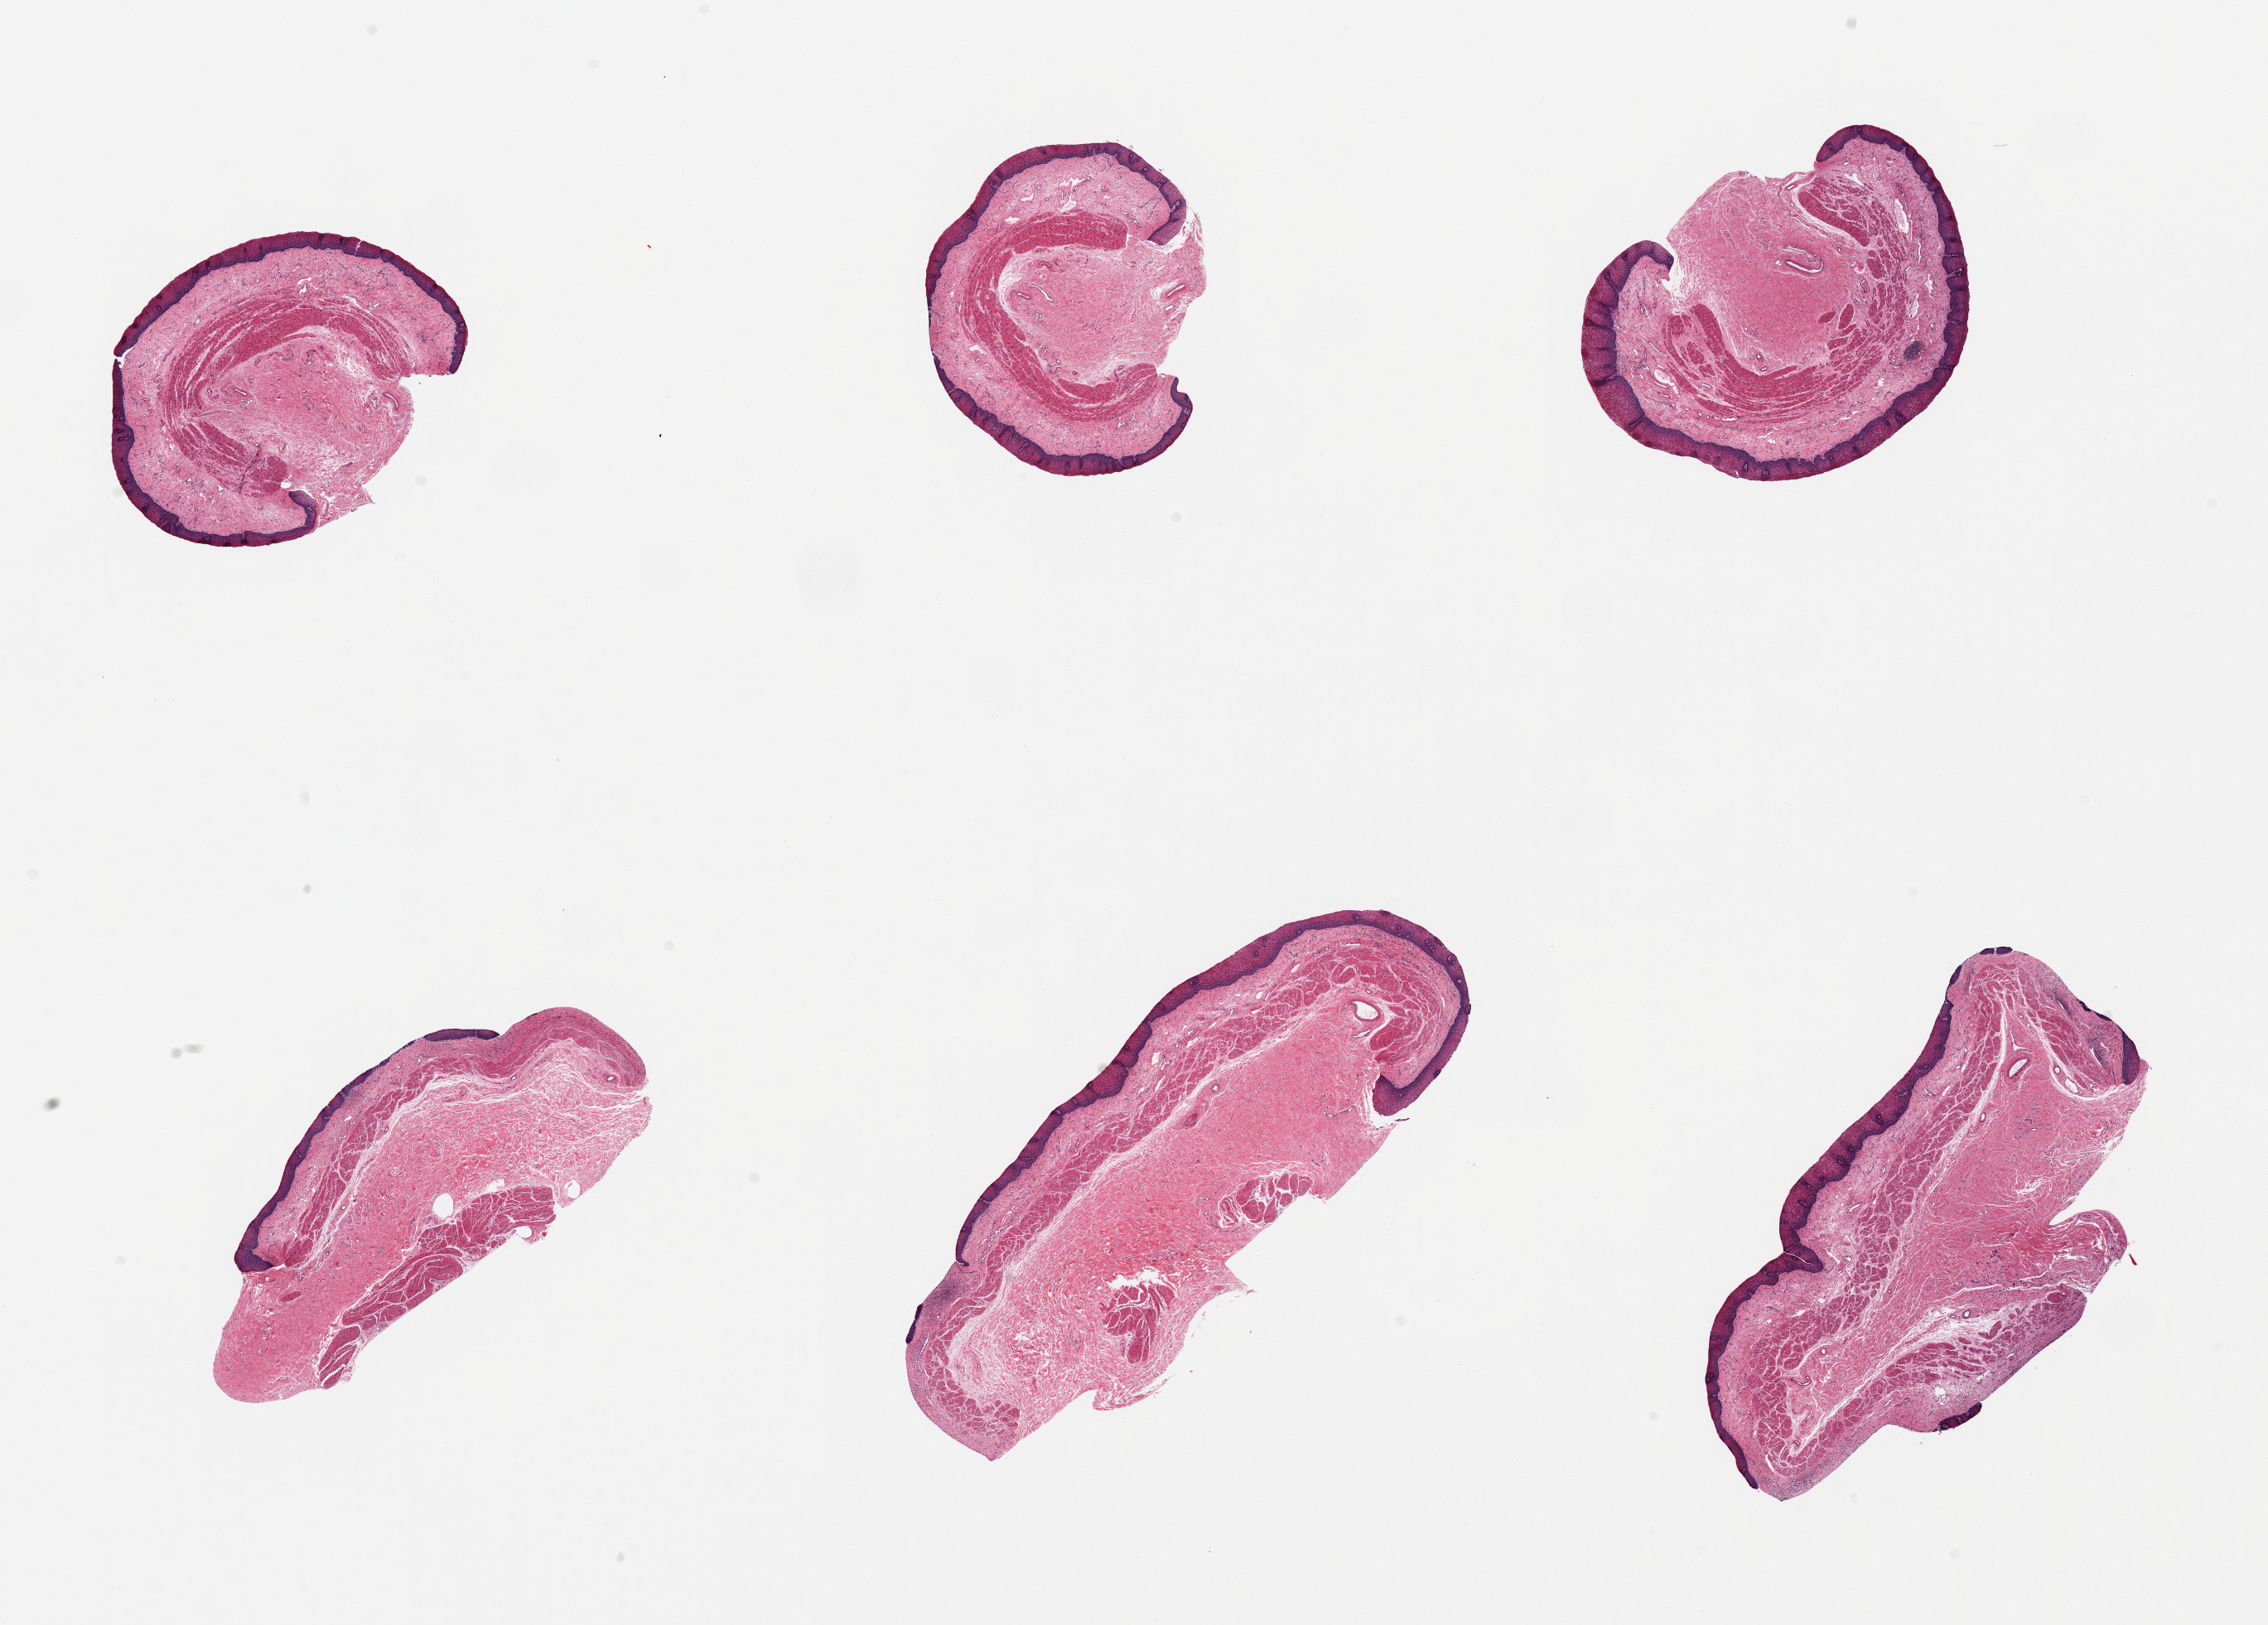
Whole-slide image, haematoxylin and eosin stain, whole scanned area (about 21.7 x 15.5 mm, from a 20x scan) shown as a low-resolution overview, PAXgene-fixed paraffin-embedded (PFPE) section, target tissue: esophageal mucous membrane, donor tissue sample.
- reviewer comment on this tissue sample: 6 pieces; well preserved